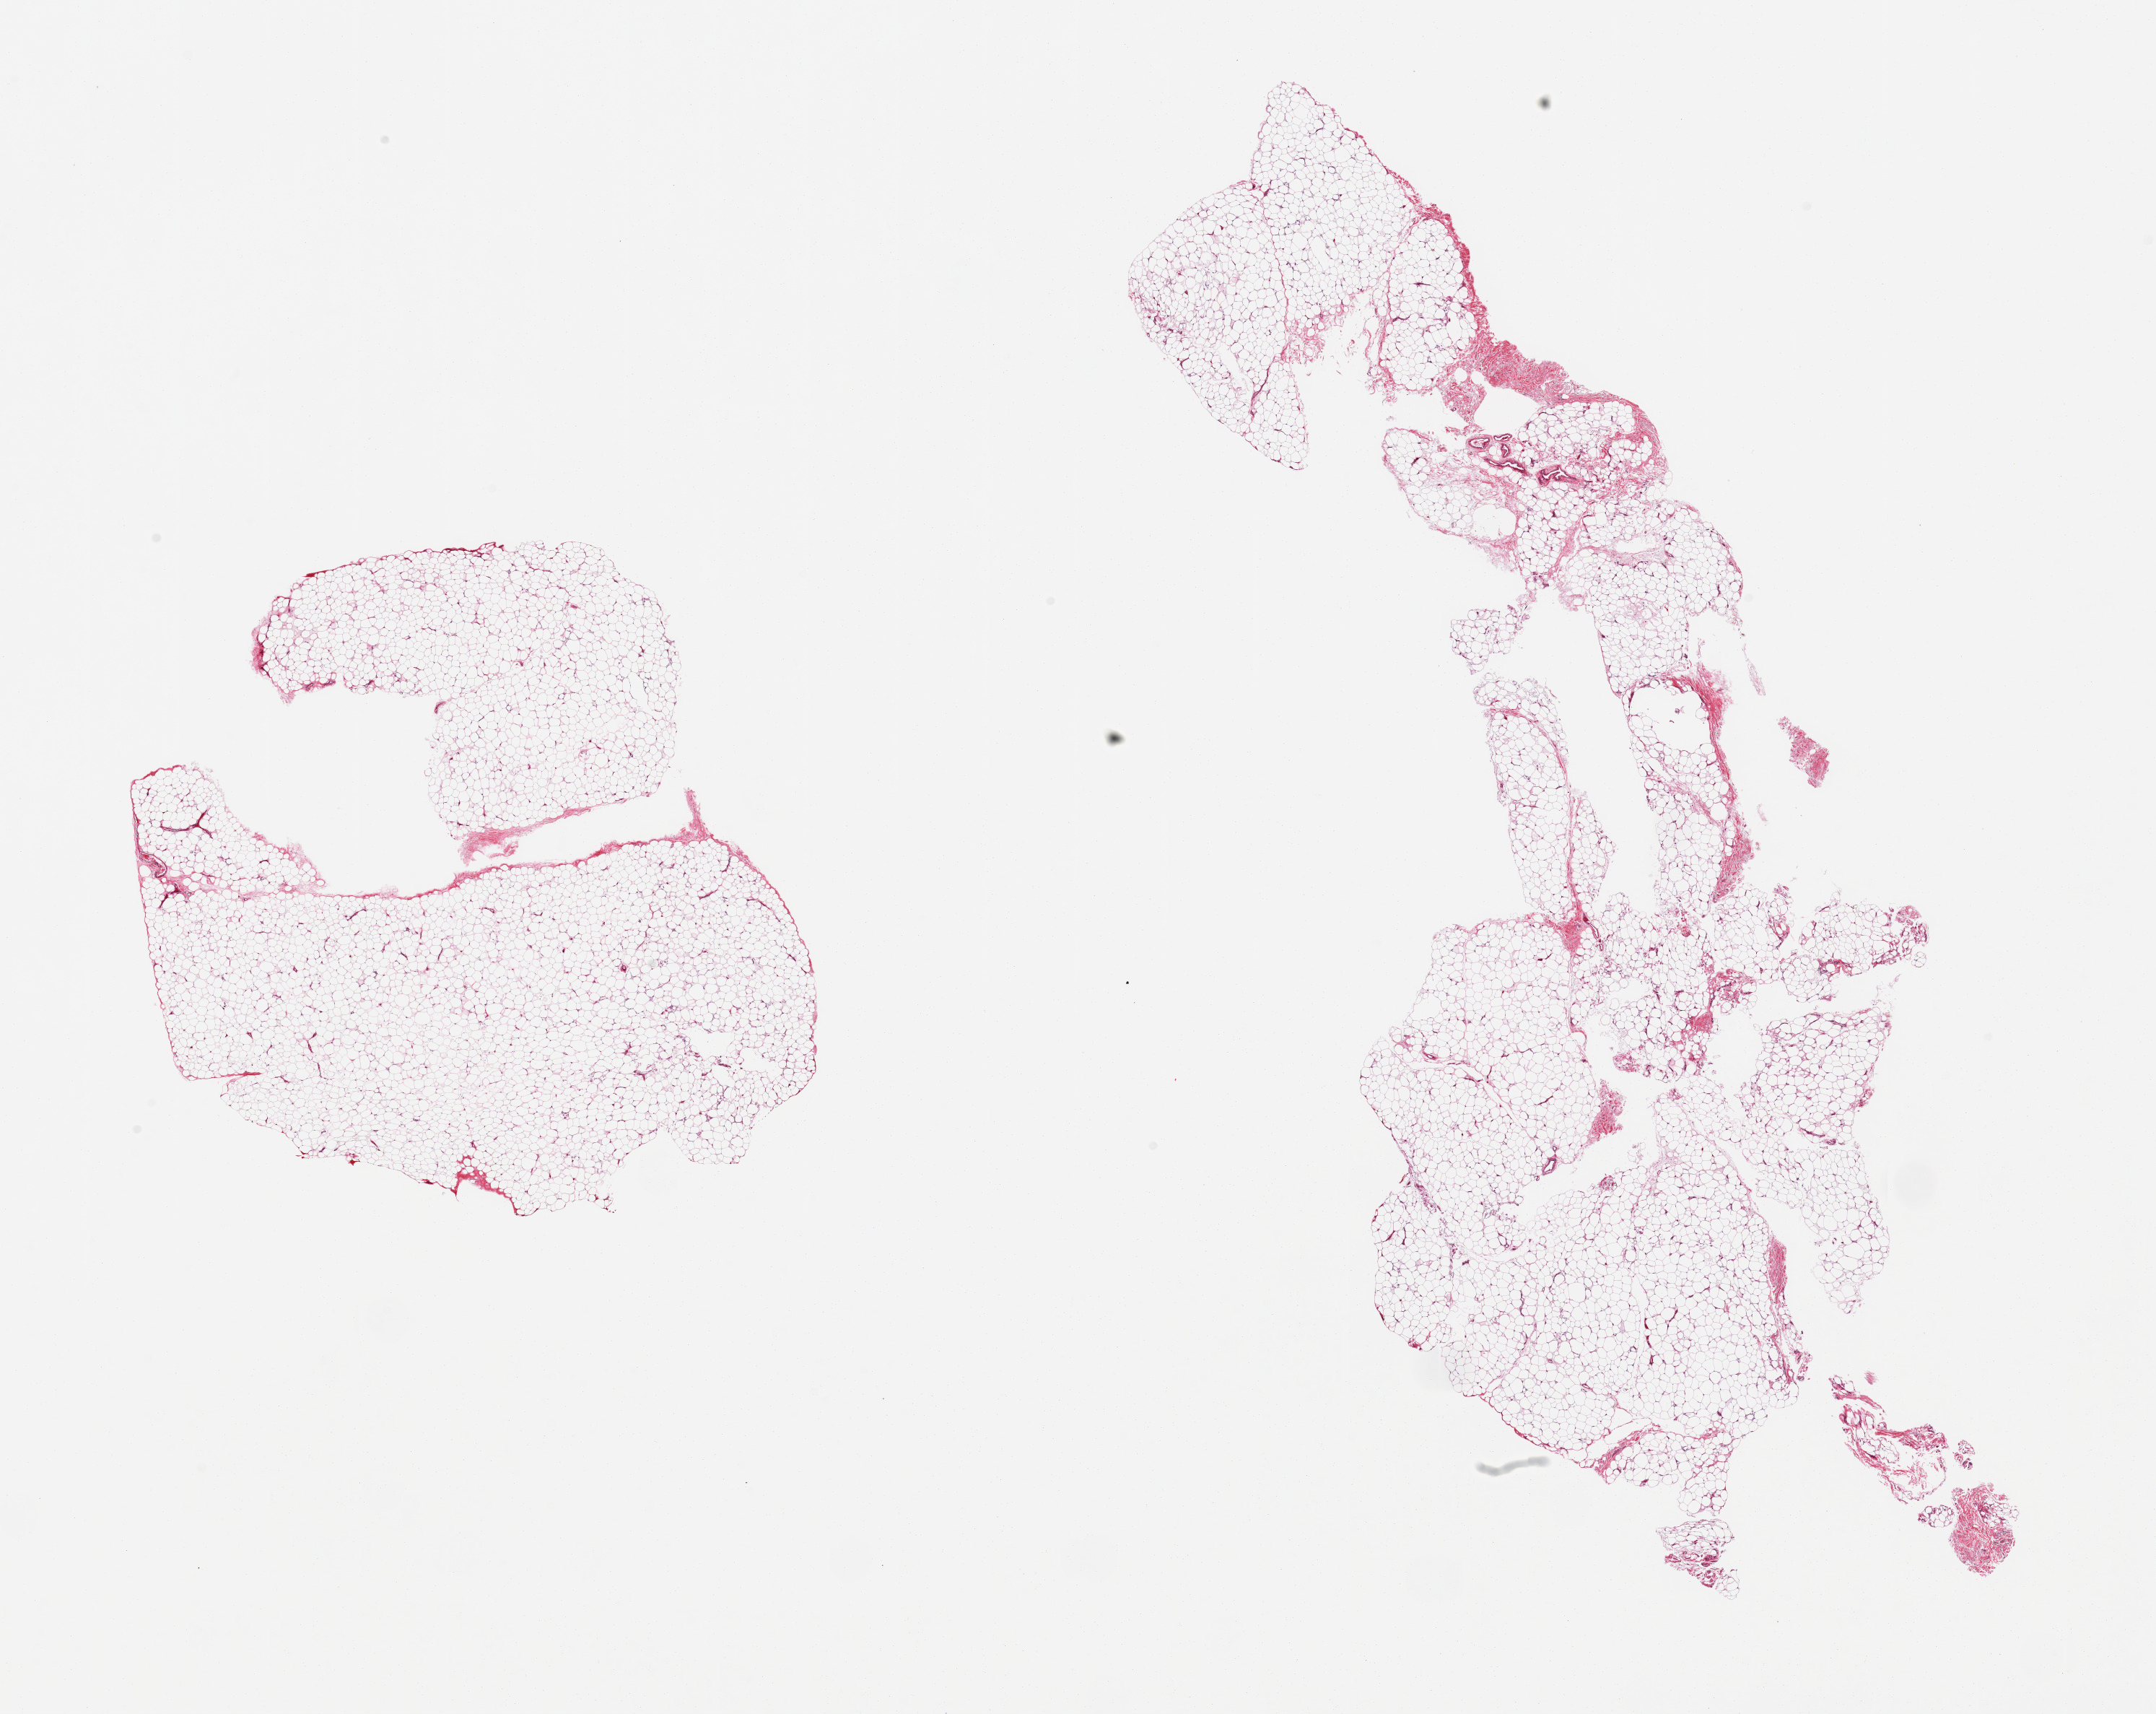
H&E whole-slide image, shown as a low-resolution overview of the whole scanned area (about 23.6 x 18.8 mm, acquisition: 20x scan). PAXgene-fixed paraffin-embedded (PFPE) section. Section of adipose tissue (target tissue). Tissue donor sample. Male donor.
Review note (as recorded): 2 pieces, <10% fascia.